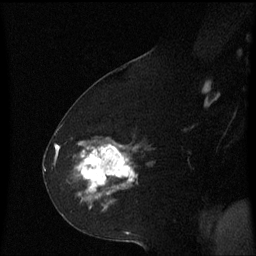
Breast MRI (dynamic contrast-enhanced), one sagittal slice. Position 32 of 60 along the scan axis. Dynamic contrast-enhanced series, image 2 of 3 at this slice position (ordered by acquisition). 1.5 T. TE 4.2 ms, TR 8.4 ms. 2.2 mm slice thickness. 256 × 256 image matrix, field of view 200 × 200 mm. Female patient, age 60 years. Case-level facts recorded for this patient, not image findings: setting: breast cancer imaged before/during neoadjuvant chemotherapy; receptor status: triple-negative.
Outlined on this slice (semi-automatic segmentation, software-assisted and operator-edited):
- analysis volume of interest (the breast-tissue region the enhancement analysis was run in; not a lesion): bounding box [x1, y1, x2, y2] px = [75, 142, 139, 213]
- tumour enhancement mask (voxels above the 70 % enhancement threshold inside the analysis volume of interest): [77, 144, 138, 195]